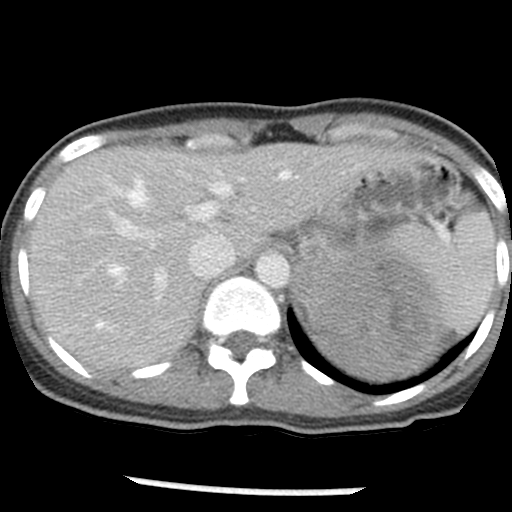
Contrast-enhanced abdominal CT, one axial slice; slice 37 of 54 in the series (ordered by position); reconstruction kernel STANDARD; intravenous contrast given; soft-tissue window (W 400 / L 40 HU); 5 mm slice thickness; 512 × 512 image matrix, field of view 240 × 240 mm. Female patient, age 33 years. From the clinical record (not read from this slice): diagnosis: adrenocortical carcinoma; tumour side: left adrenal; tumour size at pathology: 11 cm; Ki-67 index: 20 %; stage (as recorded): 2.
Annotated regions visible in this slice (semi-automatic segmentation, software-assisted and operator-edited):
- mass: box from (x=294, y=238) to (x=450, y=381) px